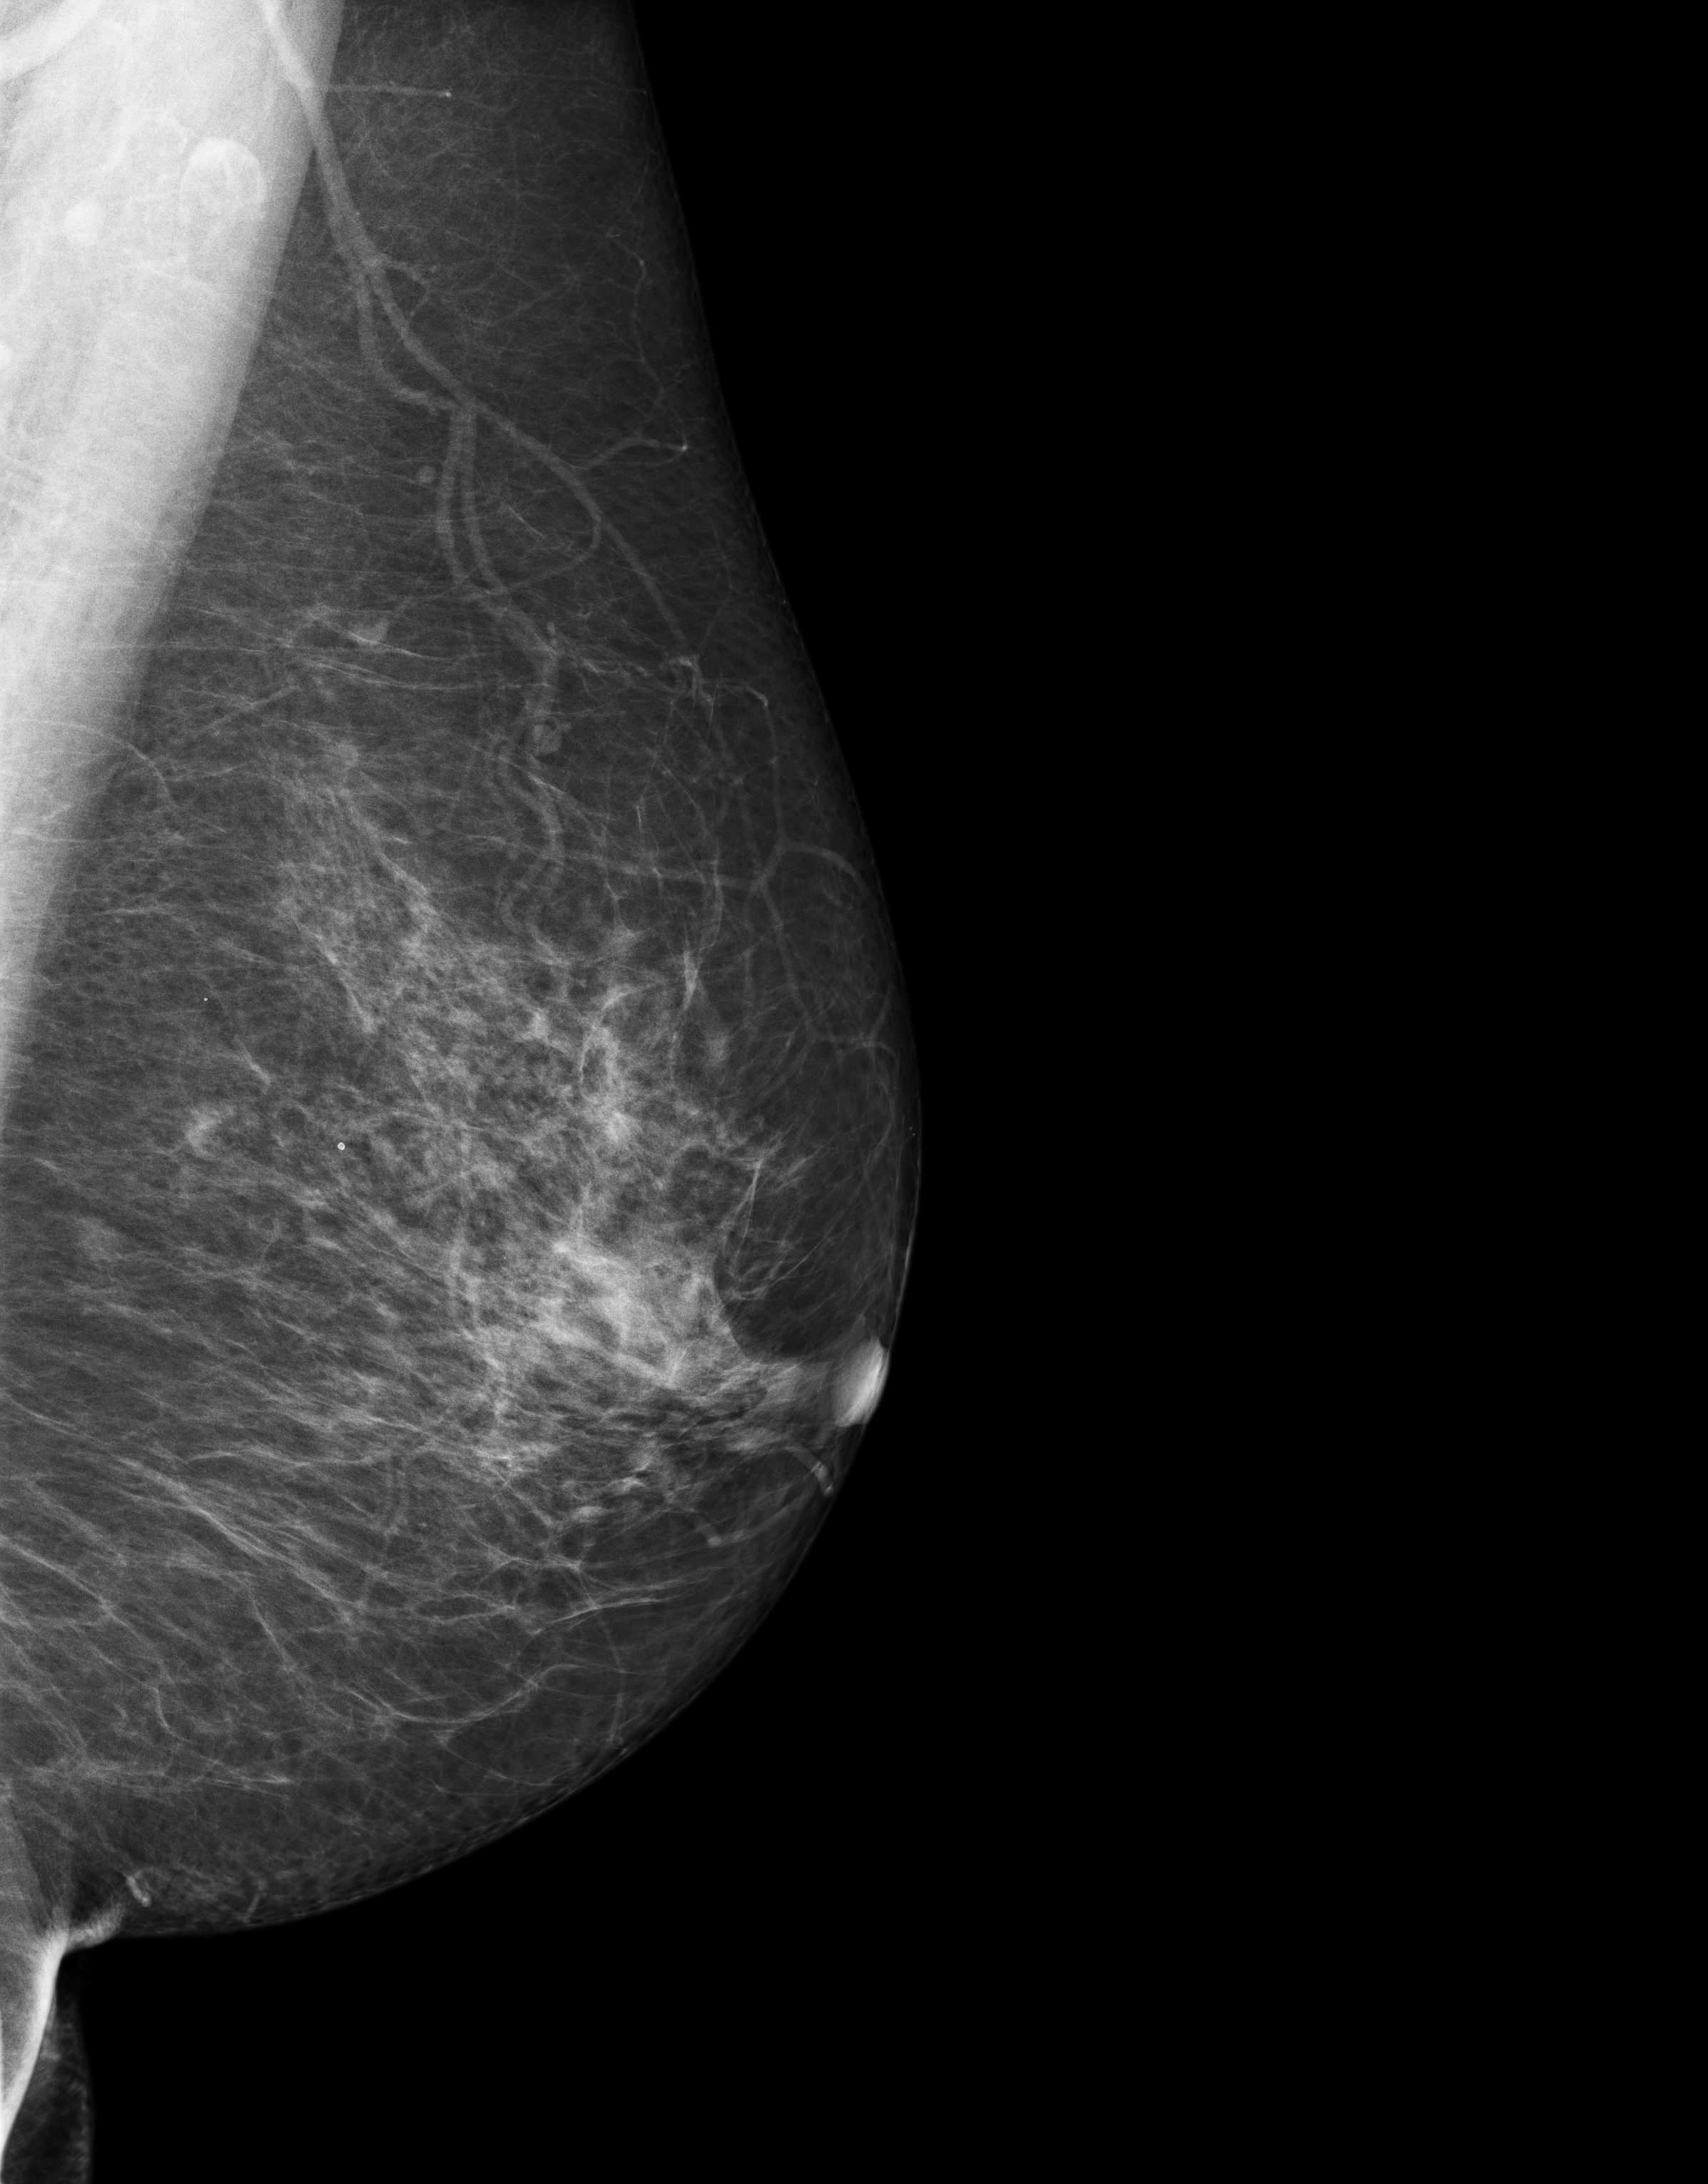
Full-field digital mammogram (FFDM), left breast, mediolateral oblique (MLO) view, screening examination, compressed breast thickness 79 mm. Female patient, age 53 years.
- breast density at the screening exam (both breasts): heterogeneously dense (BI-RADS density category c)
- final BI-RADS category for the screening round (tomosynthesis exam, both breasts): category 4
- recall: recalled for additional imaging after this screen